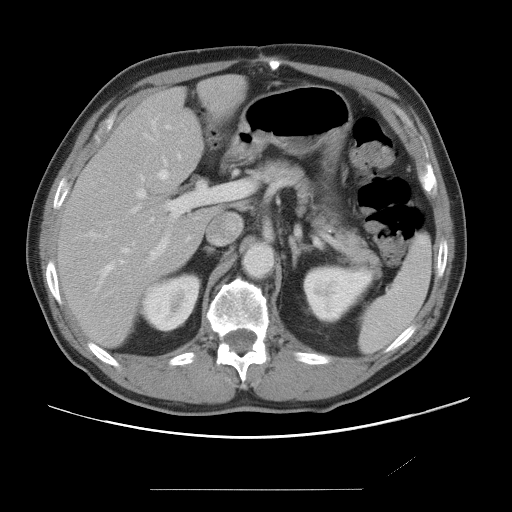
Contrast-enhanced abdominal CT, one axial slice; slice 43 of 87 in the series (ordered by position); 120 kVp; intravenous contrast given; soft-tissue window (W 400 / L 40 HU); 5 mm slice thickness; 512 × 512 image matrix, field of view 406 × 406 mm. Male patient, age 74 years. From the clinical record (not read from this slice): diagnosis: colorectal cancer liver metastases, imaged before liver resection; multiple liver metastases: yes; largest metastasis: 1.1 cm.
Annotated regions visible in this slice (manually delineated by an expert):
- hepatic veins: bounding box (x1, y1, x2, y2) in pixels: (95, 119, 181, 291)
- liver: (58, 77, 246, 347)
- planned liver remnant (the part of the liver to remain after resection): (58, 77, 246, 347)
- portal vein (with intrahepatic branches): (131, 176, 253, 259)